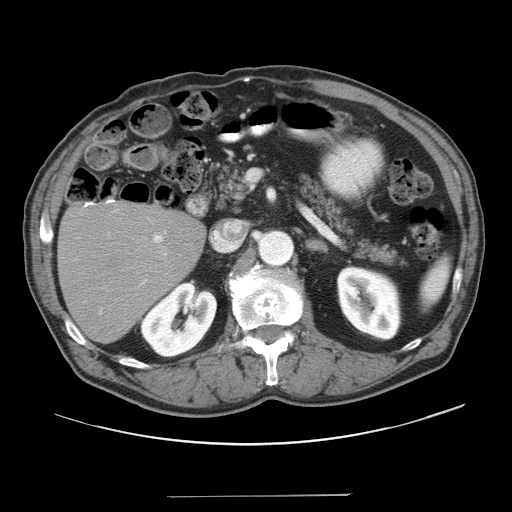
Contrast-enhanced abdominal CT, one axial slice. Position 19 of 41 along the scan axis. Soft-tissue window (W 400 / L 40 HU). 5 mm slice thickness. 512 × 512 image matrix, field of view 420 × 420 mm. Male patient, age 75 years. From the clinical record (not read from this slice): diagnosis: colorectal cancer liver metastases, imaged before liver resection; multiple liver metastases: no; largest metastasis: 5.2 cm; disease in both lobes: no.
Annotated regions visible in this slice (outlined manually by an expert reader):
- liver: box from (x=60, y=204) to (x=203, y=343) px
- planned liver remnant (the part of the liver to remain after resection): (x=60, y=204)–(x=203, y=342)
- portal vein (with intrahepatic branches): (x=99, y=209)–(x=167, y=315)